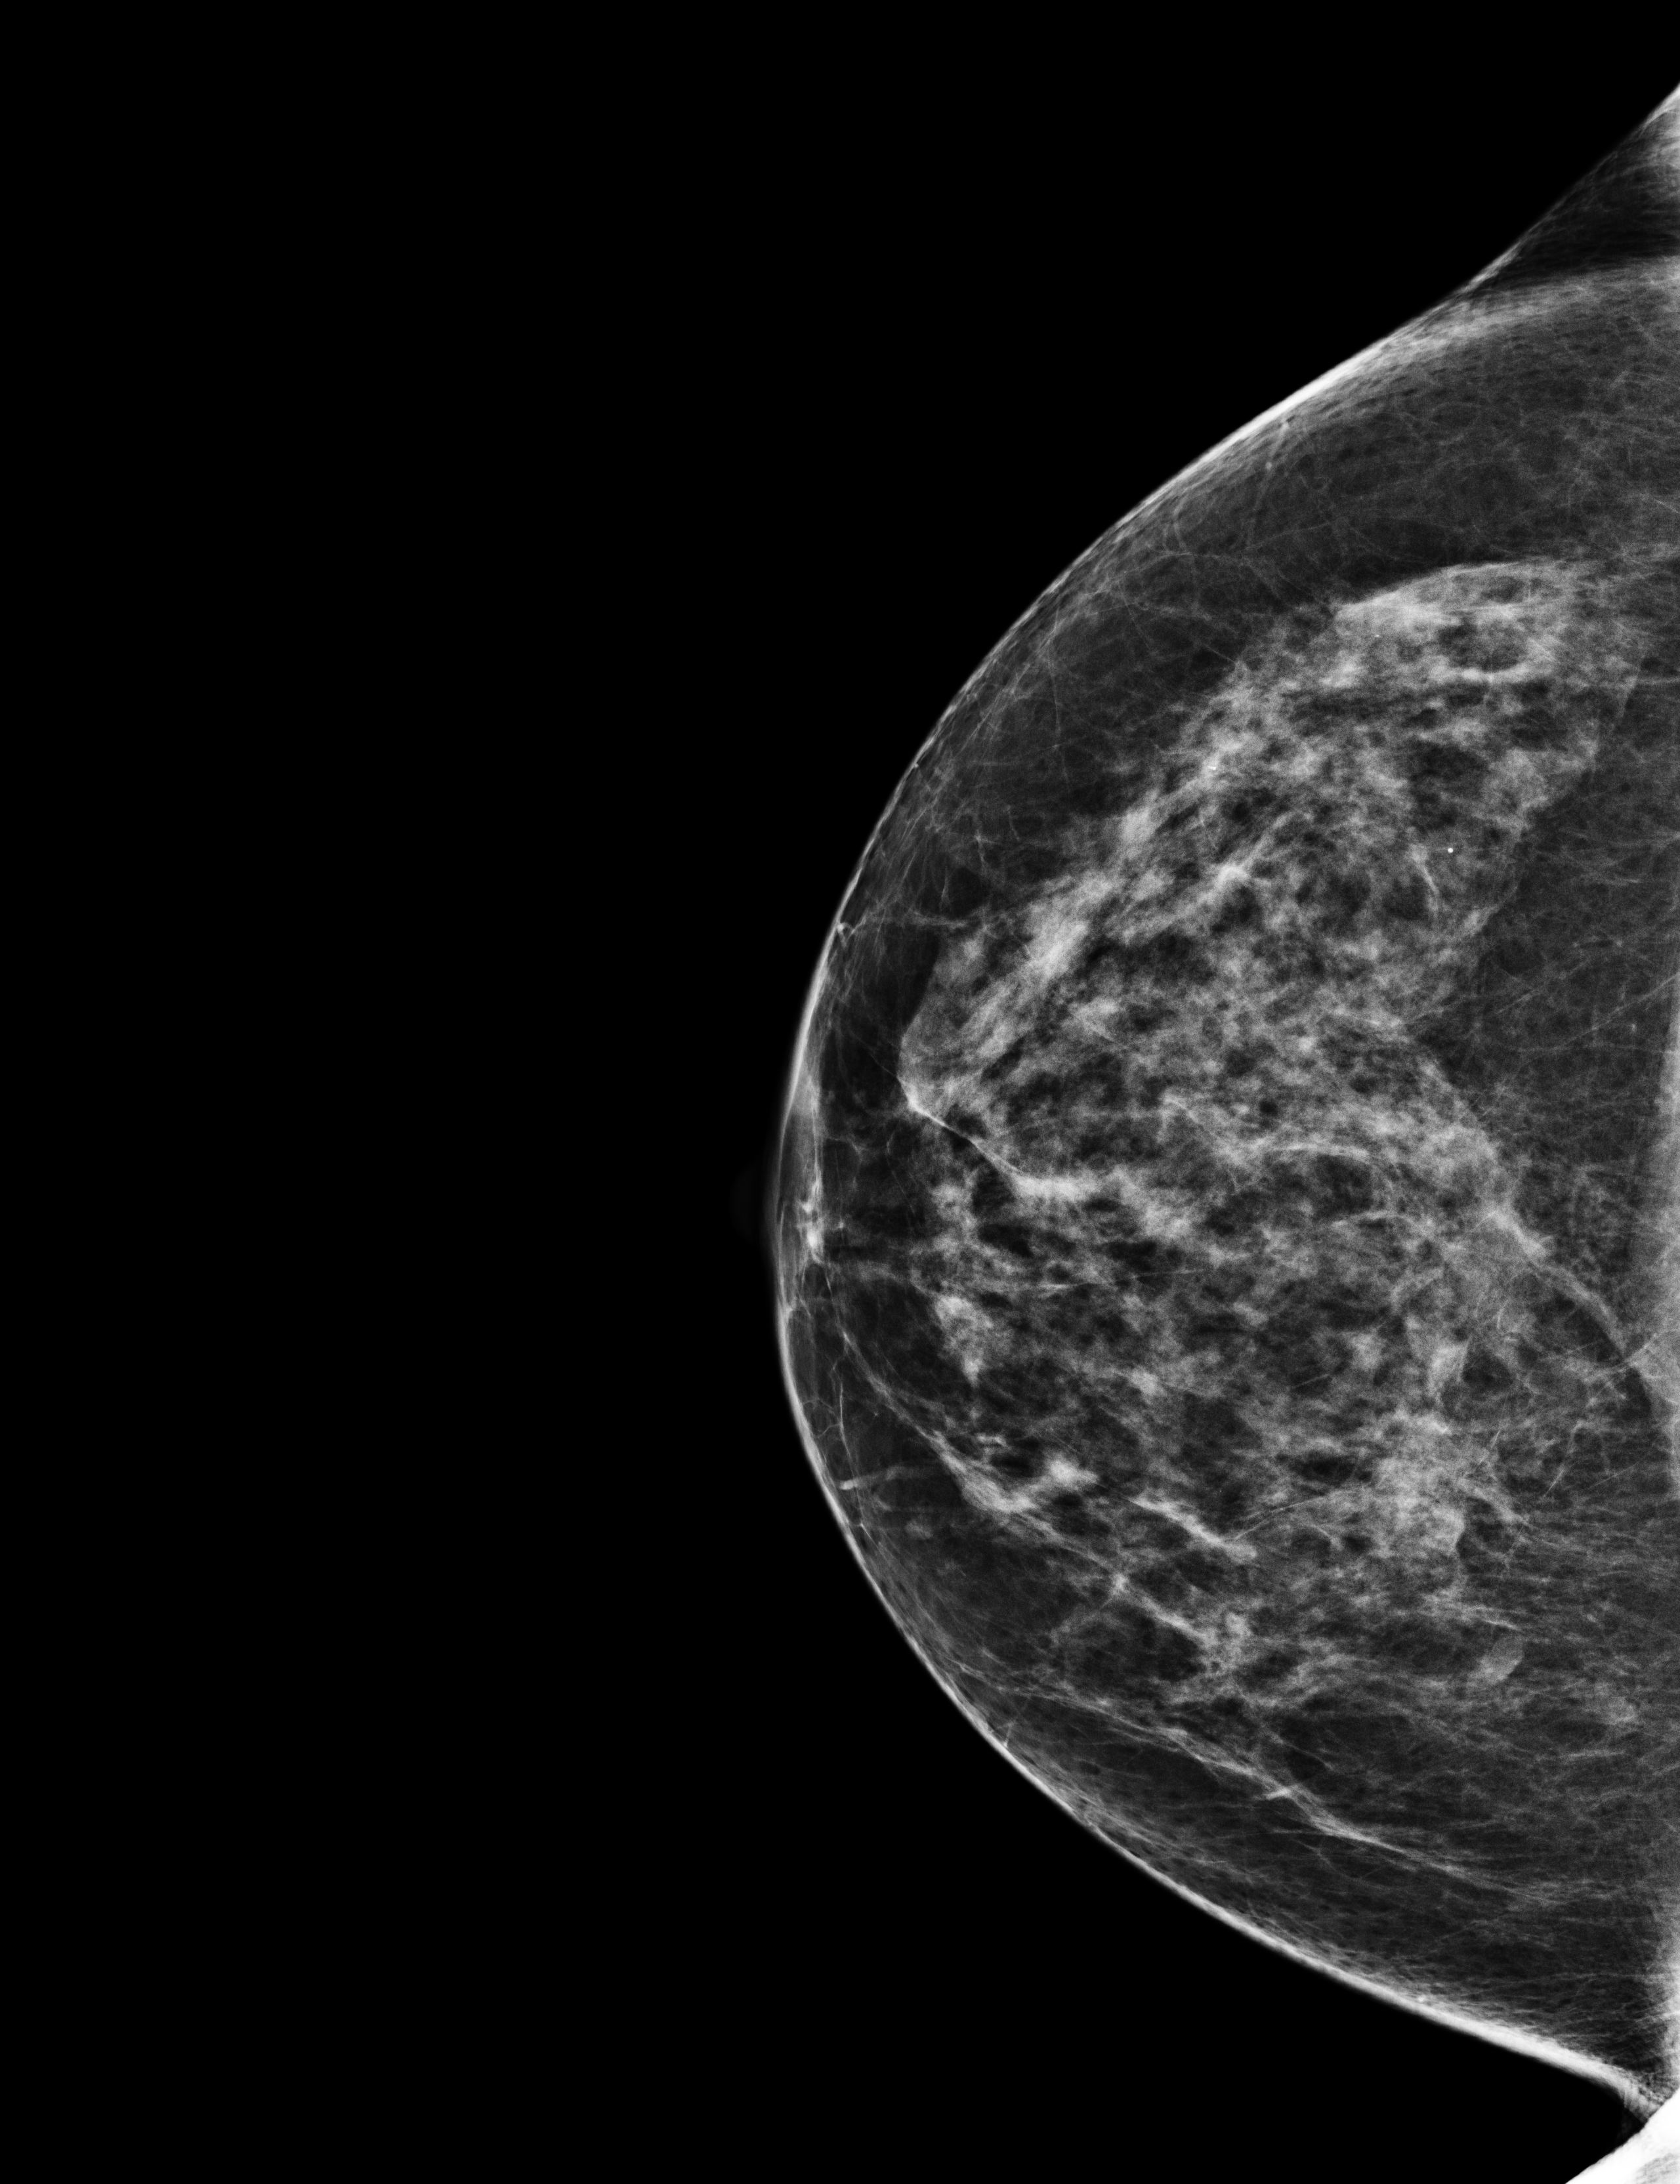
Full-field digital mammogram (FFDM), right breast, craniocaudal (CC) view, annual screening mammography examination, compressed breast thickness 64 mm. Patient: female, 60 years.
BI-RADS breast density category at the screening exam (both breasts, scale 1–4): 3. Final BI-RADS category for the screening round (tomosynthesis exam, both breasts): category 1. Recall: no recall after this screen.